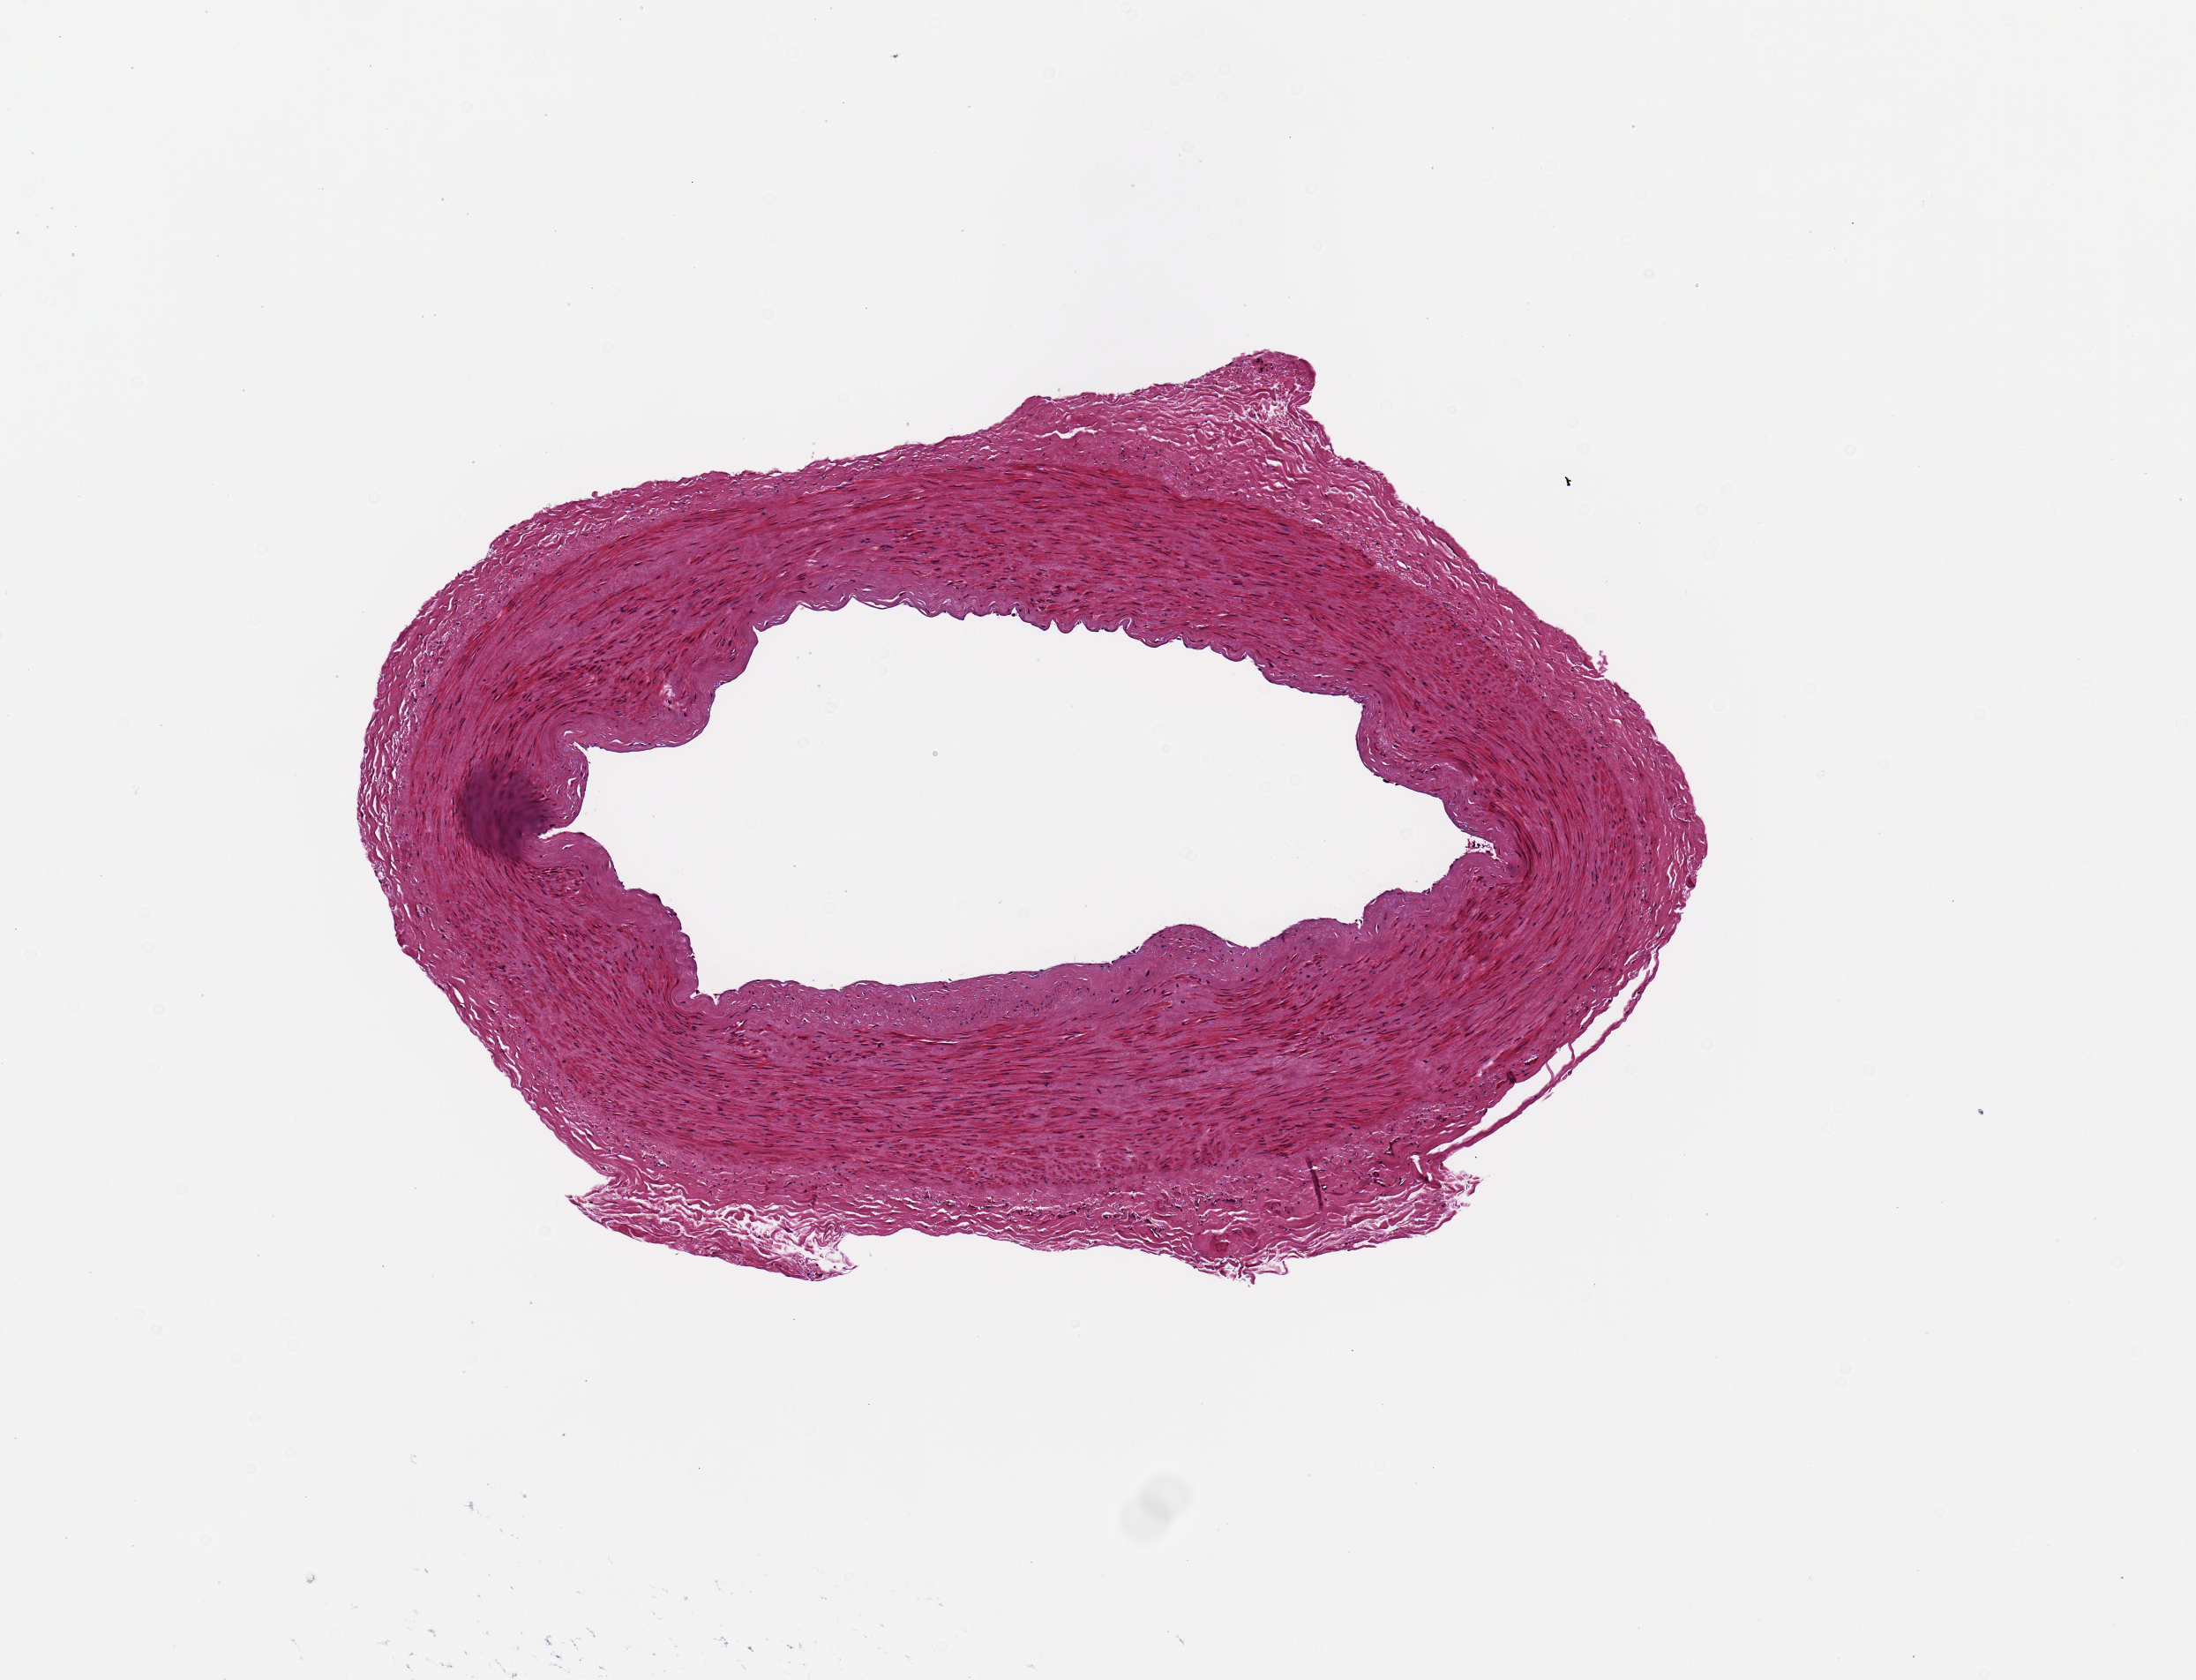
Hematoxylin and eosin (H&E) whole-slide image, a low-resolution overview of the entire scanned area, about 4.9 x 3.8 mm (from a 20x scan), PAXgene-fixed, paraffin-embedded tissue, section of tibial artery (target tissue), tissue donor sample. Donor: male.
• review note (as recorded): Minimal intimal thickening